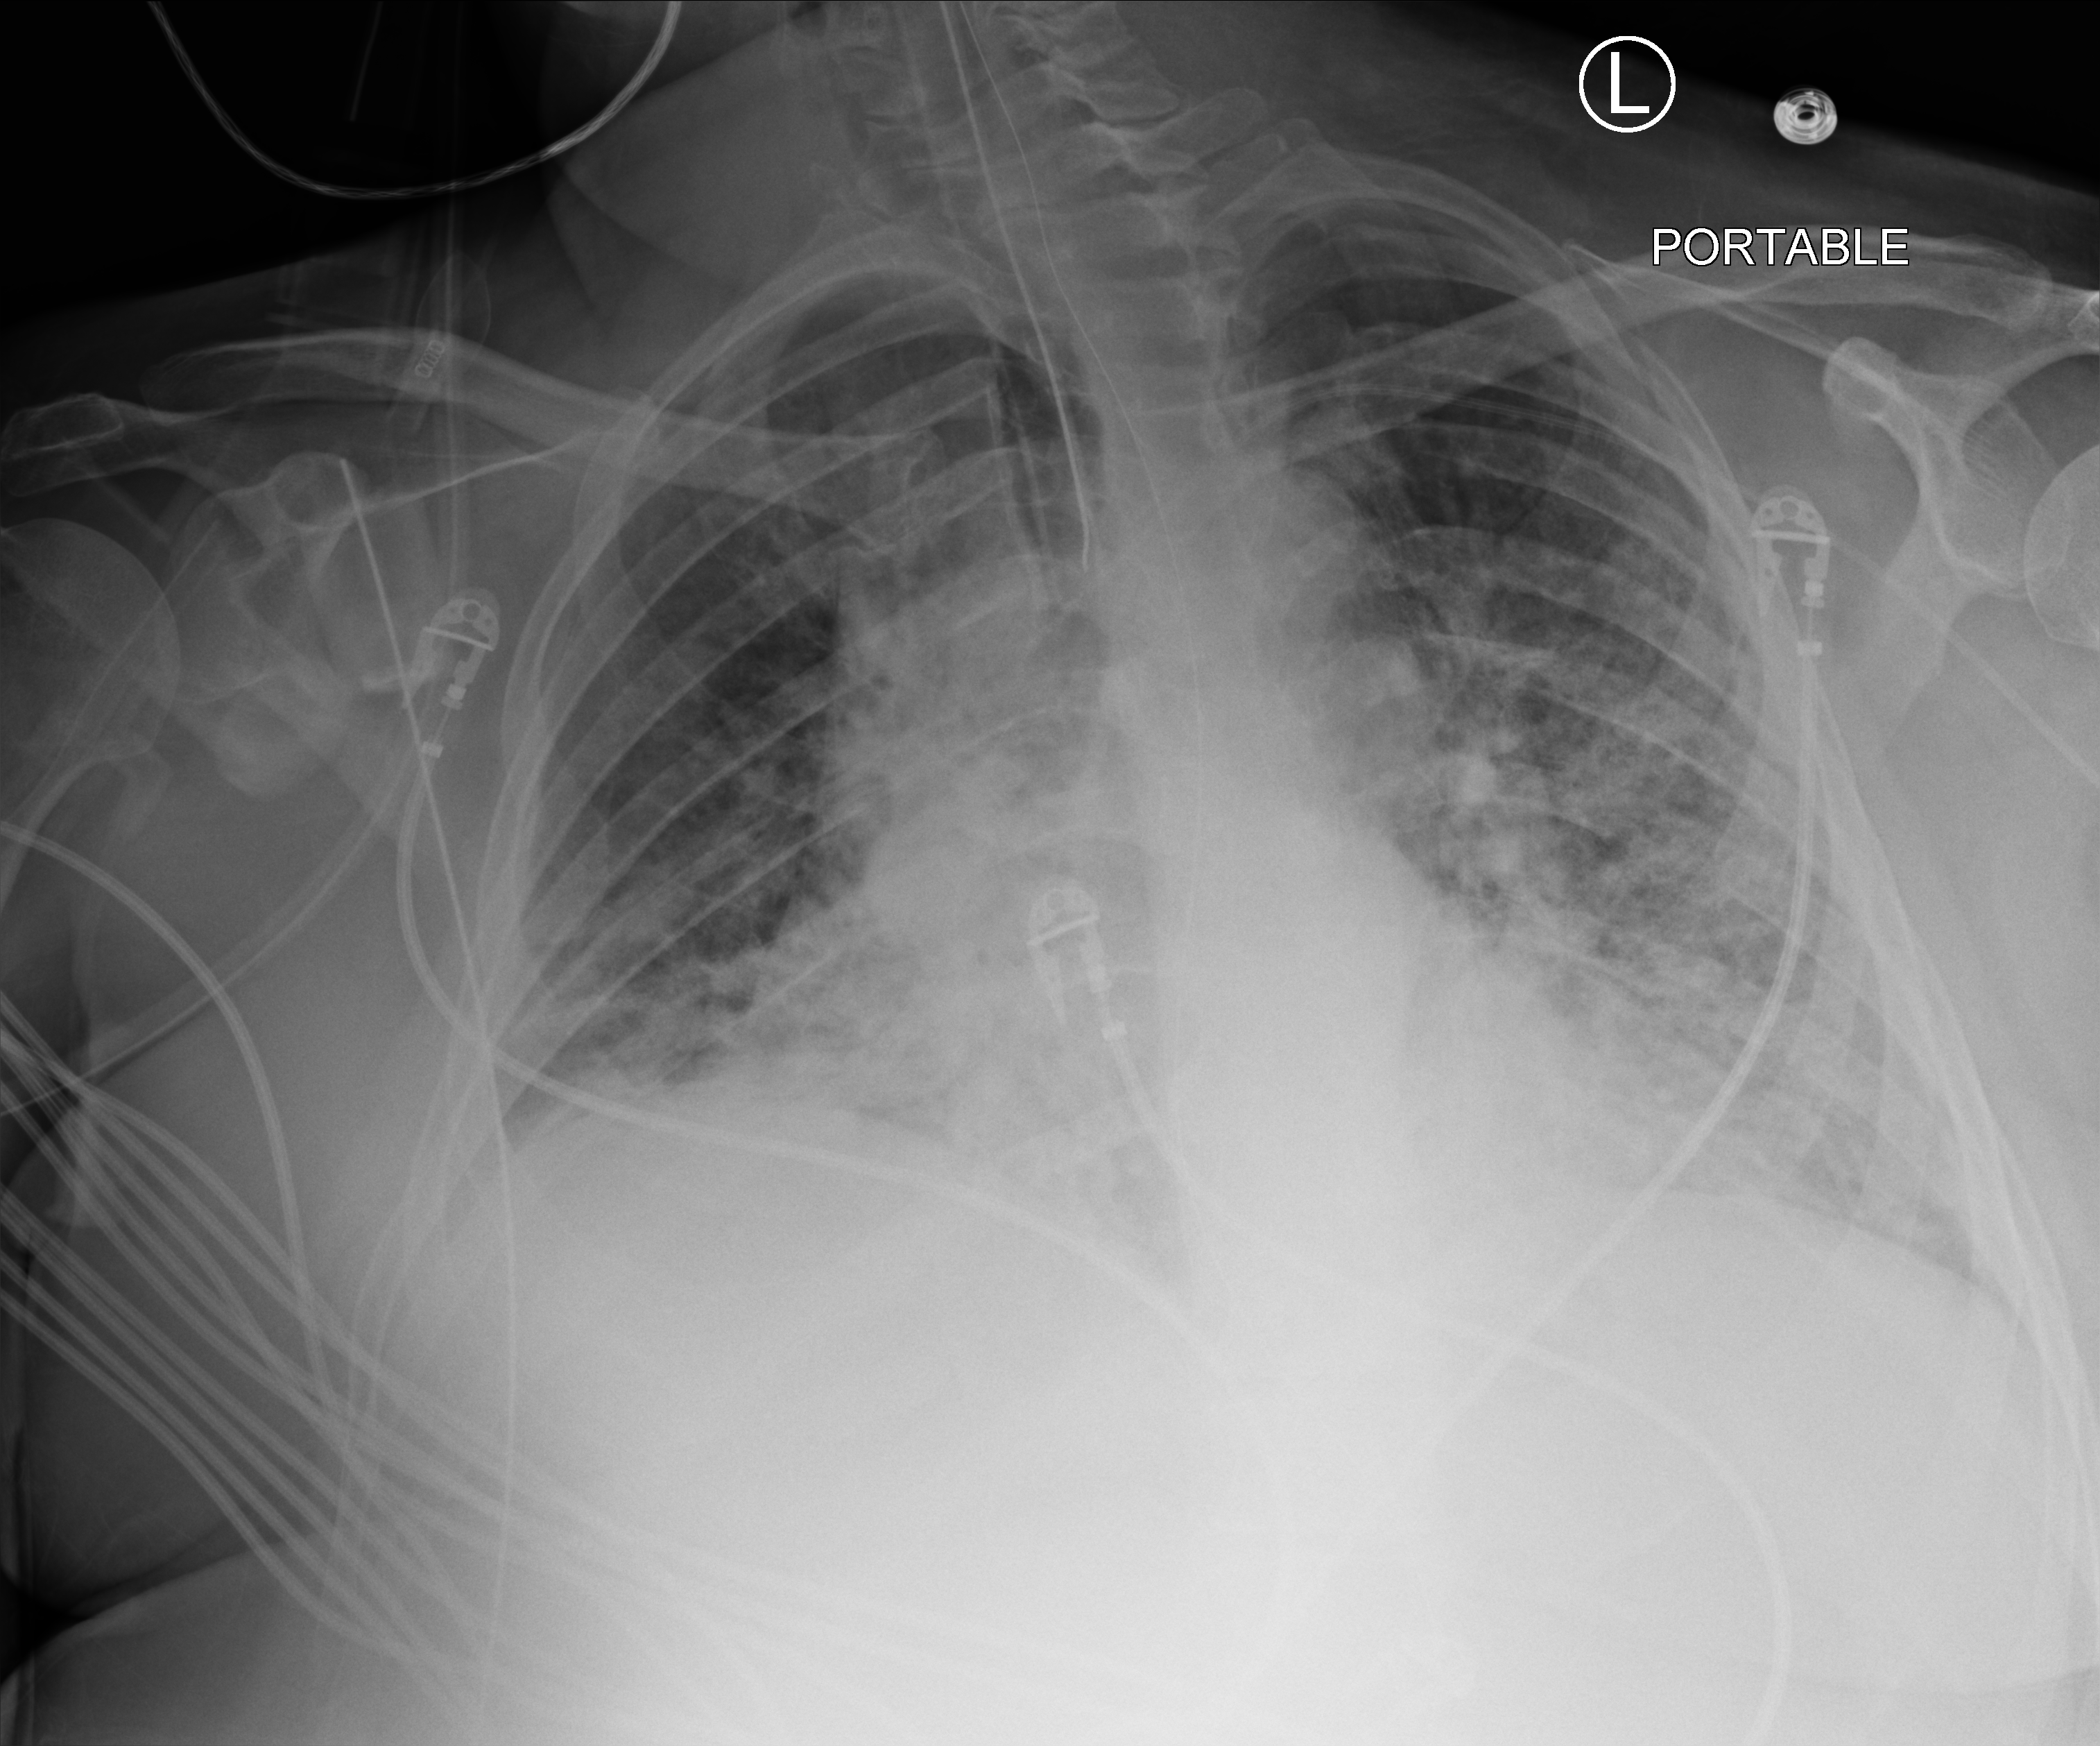
Portable chest radiograph; anteroposterior (AP) projection. Patient hospitalised with COVID-19; male, aged 18–59 years.
From the hospital-stay record, not from the radiograph (when in the stay this image was taken is not recorded): admitted to intensive care during this hospital stay: yes.